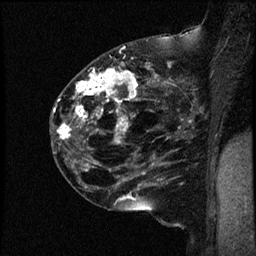
Breast MRI (dynamic contrast-enhanced), one sagittal slice; slice 29 of 44 in the series (ordered by position); dynamic contrast-enhanced study with each time point stored as its own series, time point 2 of 4 at this slice position (early post-contrast, ordered by acquisition time); 1.5 T; TE 4.2 ms, TR 17.7 ms; 2 mm slice thickness; 256 × 256 image matrix. Female patient, age 52 years. Case-level facts recorded for this patient, not image findings: setting: breast cancer imaged before/during neoadjuvant chemotherapy; receptor status: HR-positive, HER2-negative.
Annotated regions visible in this slice (semi-automatic segmentation, software-assisted and operator-edited):
- analysis volume of interest (the breast-tissue region the enhancement analysis was run in; not a lesion): bounding box <50,48,163,147> (left, top, right, bottom; pixels)
- tumour enhancement mask (voxels above the 100 % enhancement threshold inside the analysis volume of interest): <57,68,138,144>